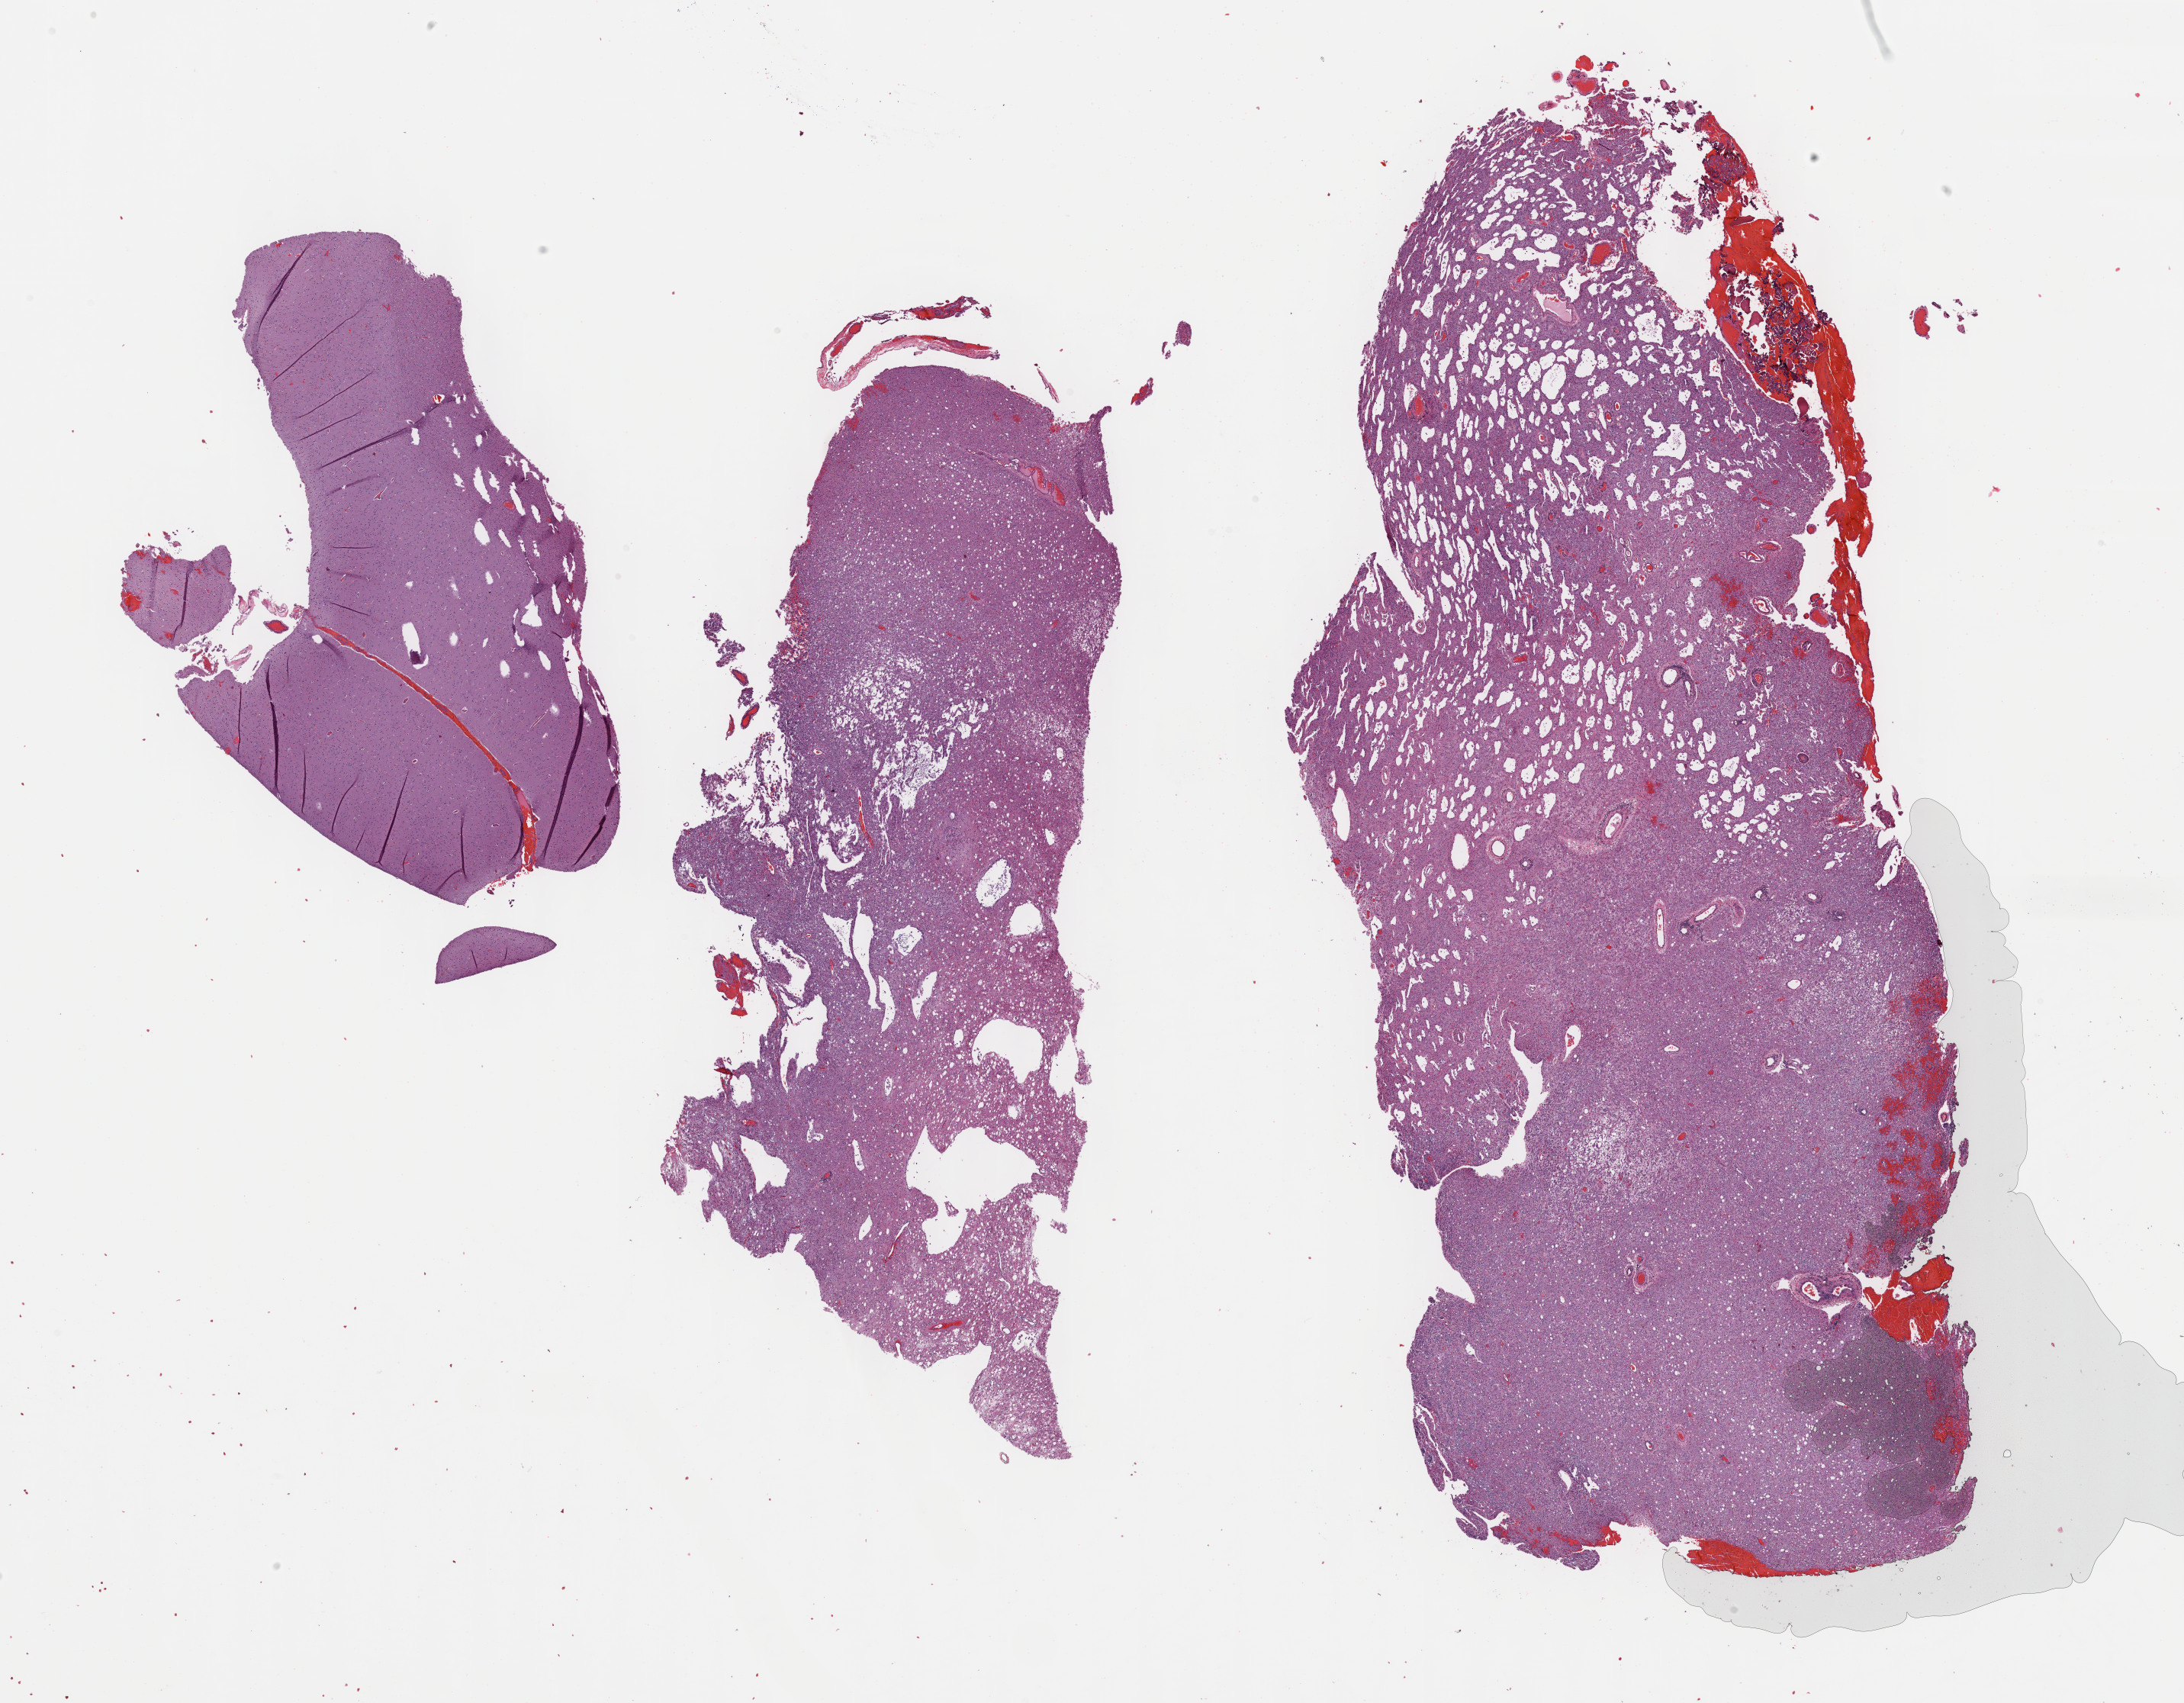
Digitized H&E-stained tissue section (whole slide), whole scanned area (about 23.2 x 18.1 mm) shown as a low-resolution overview; formalin-fixed paraffin-embedded (FFPE) diagnostic section; primary tumour sample from the brain. Patient: male, age at initial diagnosis 35 years. Histologic grade: G3 (poorly differentiated).
Laterality: left. Diagnosis: Oligodendroglioma, anaplastic (cerebrum).